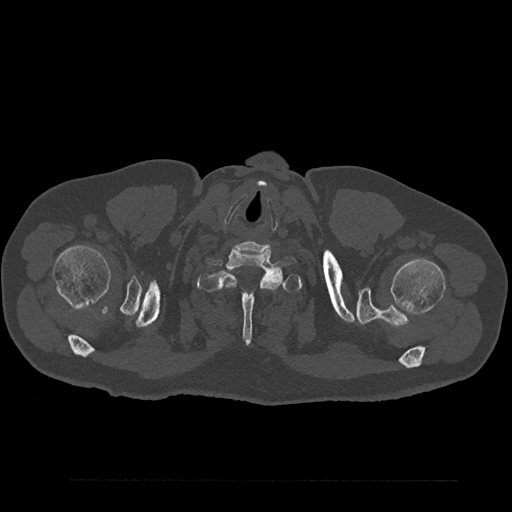
CT including the spine, one axial slice; position 768 of 797 along the scan axis; reconstruction kernel Br40s/3; 120 kVp; bone window (W 1800 / L 400 HU); 0.5 mm slice thickness; 512 × 512 image matrix, field of view 430 × 430 mm. Patient: male, 61 years. From the clinical record (not read from this slice): primary cancer: prostate.
Structures marked on this image (semi-automatically segmented with operator editing):
- T1 vertebra: bounding box (x1, y1, x2, y2) in pixels: (197, 261, 302, 345)